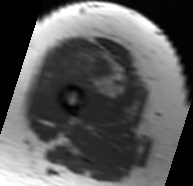
MRI of an extremity soft-tissue mass, one axial slice. Position 23 of 91 along the scan axis. MR volume resampled by the dataset authors to the PET/CT grid (not the native acquisition matrix). 3.27 mm slice thickness. 193 × 186 image matrix. Female patient. Case-level facts recorded for this patient, not image findings: histological type: malignant solitary fibrous tumor; grade: intermediate; site of the primary tumour: right thigh.
Outlined on this slice (expert contour drawn on MRI and transferred to this co-registered scan by the dataset authors):
- gross tumour volume including surrounding oedema: box from (x=58, y=37) to (x=144, y=104) px
- gross tumour volume (mass): (x=90, y=58)–(x=116, y=84)